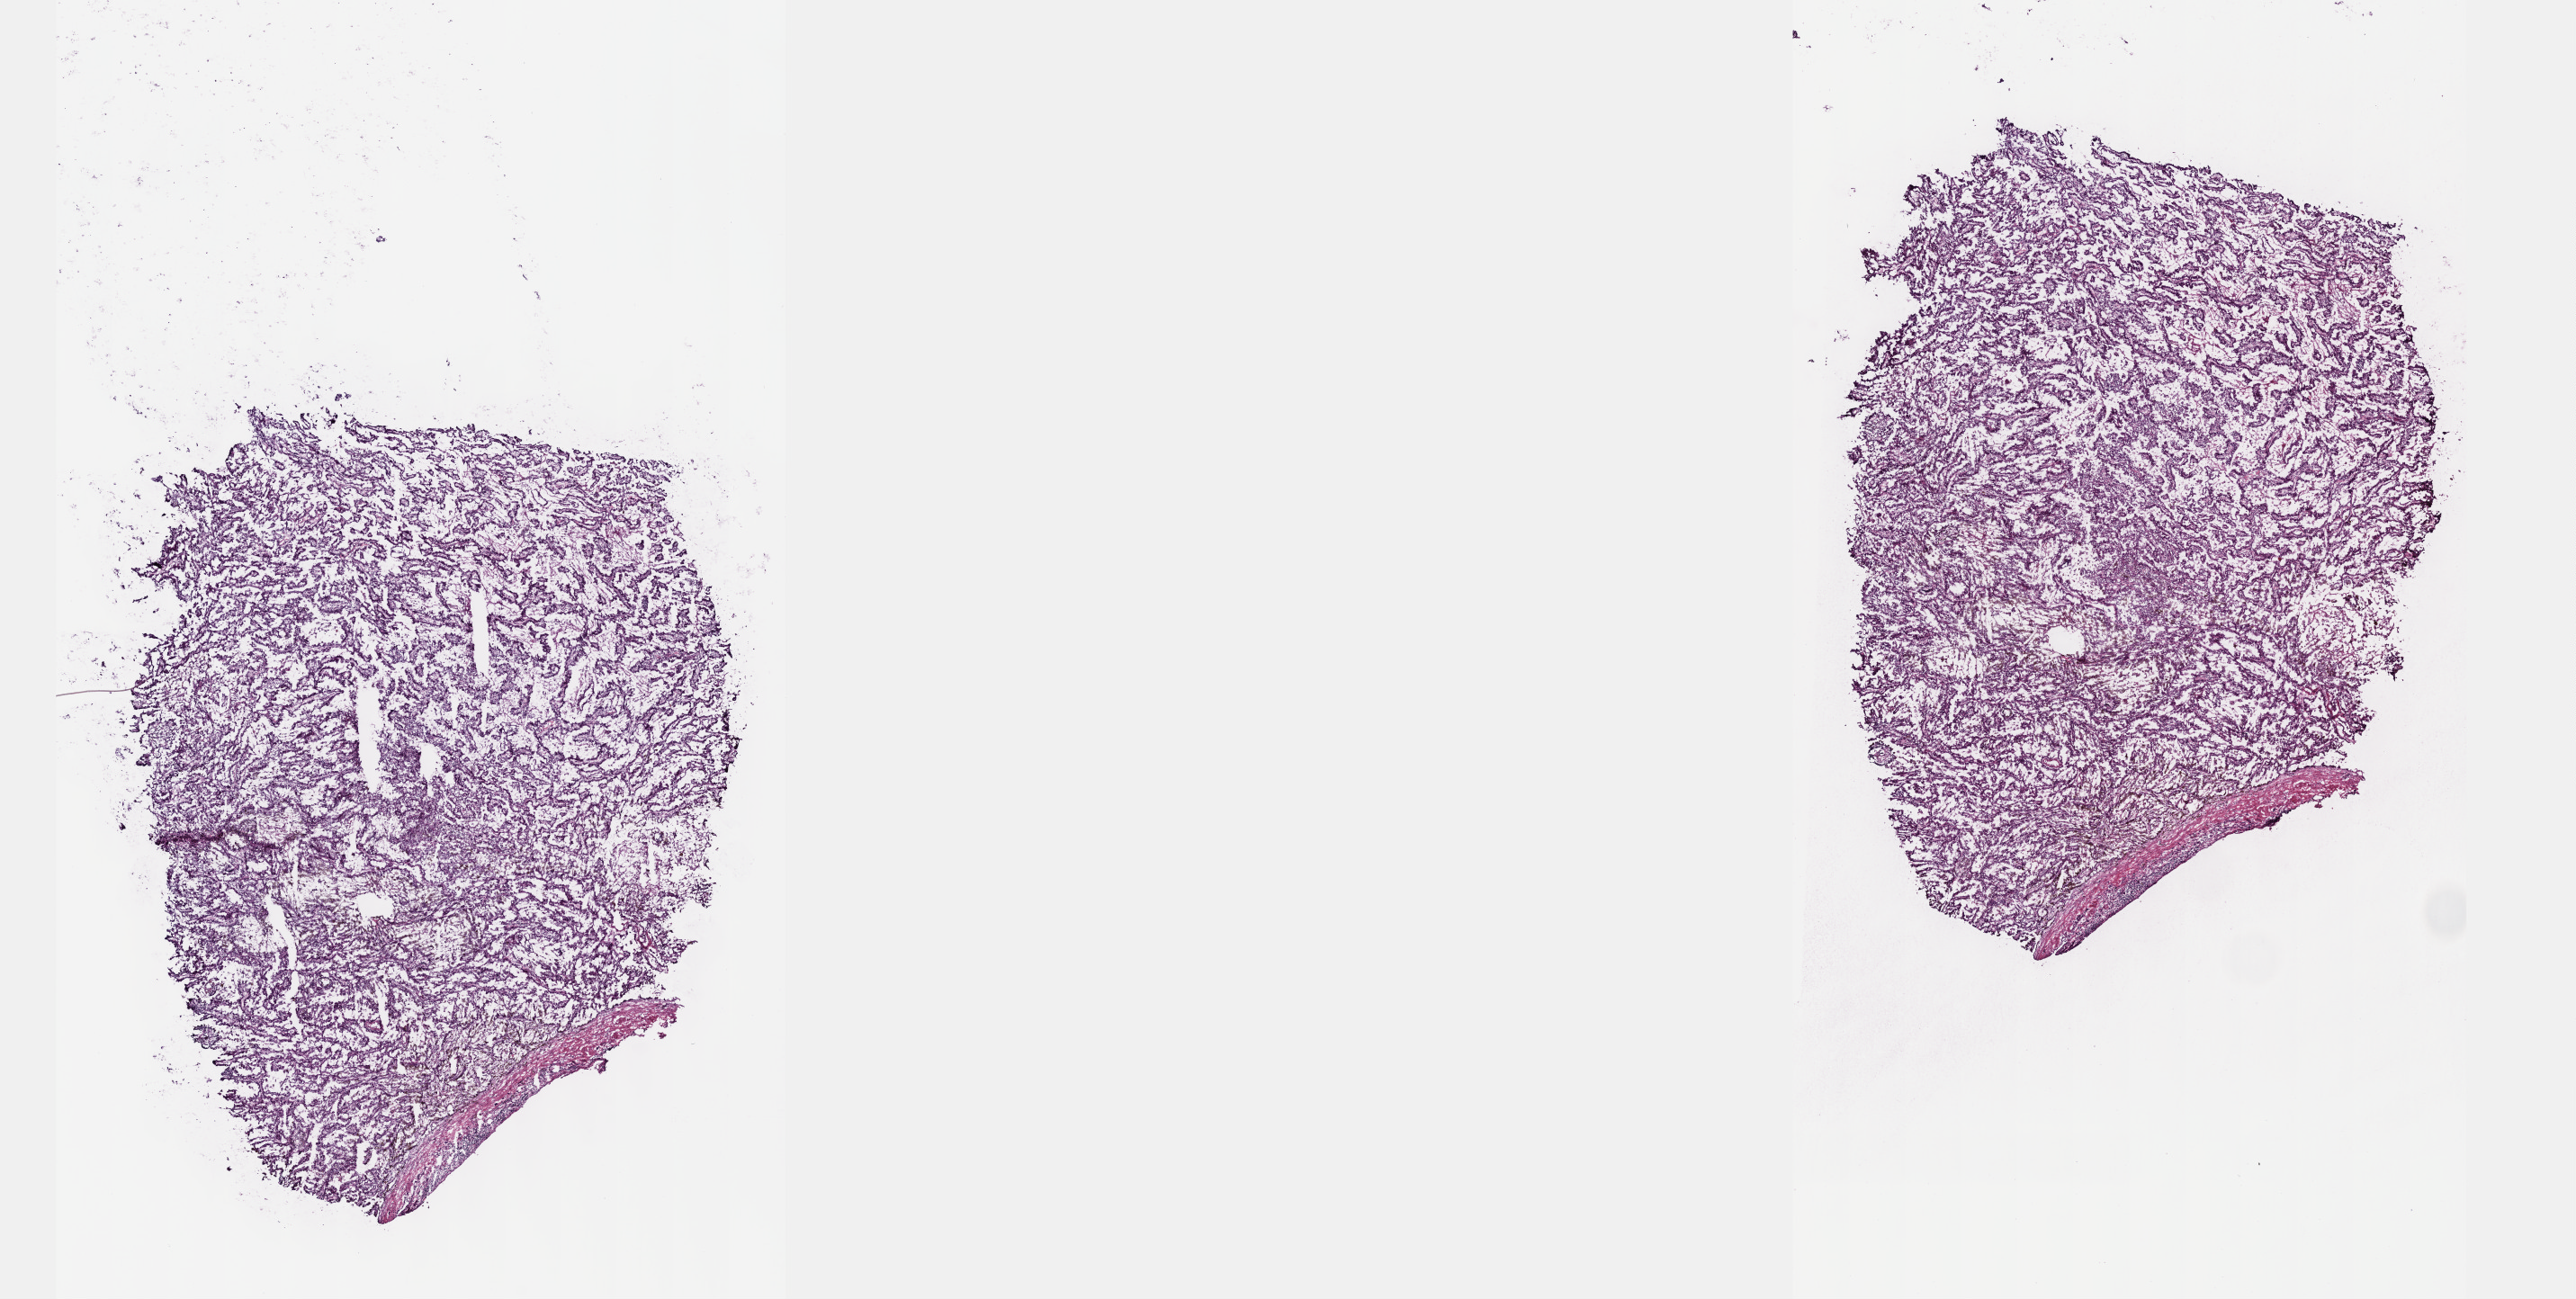
Digitized Hematoxylin and eosin (H&E) stained tissue section (whole slide), low-resolution overview of the scanned area, about 23.1 x 11.7 mm (from a 40x scan), frozen section from the top of the tissue portion, sample: primary tumour, kidney. Male patient; age at initial diagnosis 81 years. Pathologist review of this section (percent, as recorded): tumour cells 100%, tumour nuclei 70%, normal cells 0%, stromal cells 0%, necrosis 0%. Inflammatory infiltration, as recorded: lymphocyte infiltration 2%, monocyte infiltration 5%, neutrophil infiltration 0%.
- diagnosis: Papillary adenocarcinoma, NOS
- laterality: left